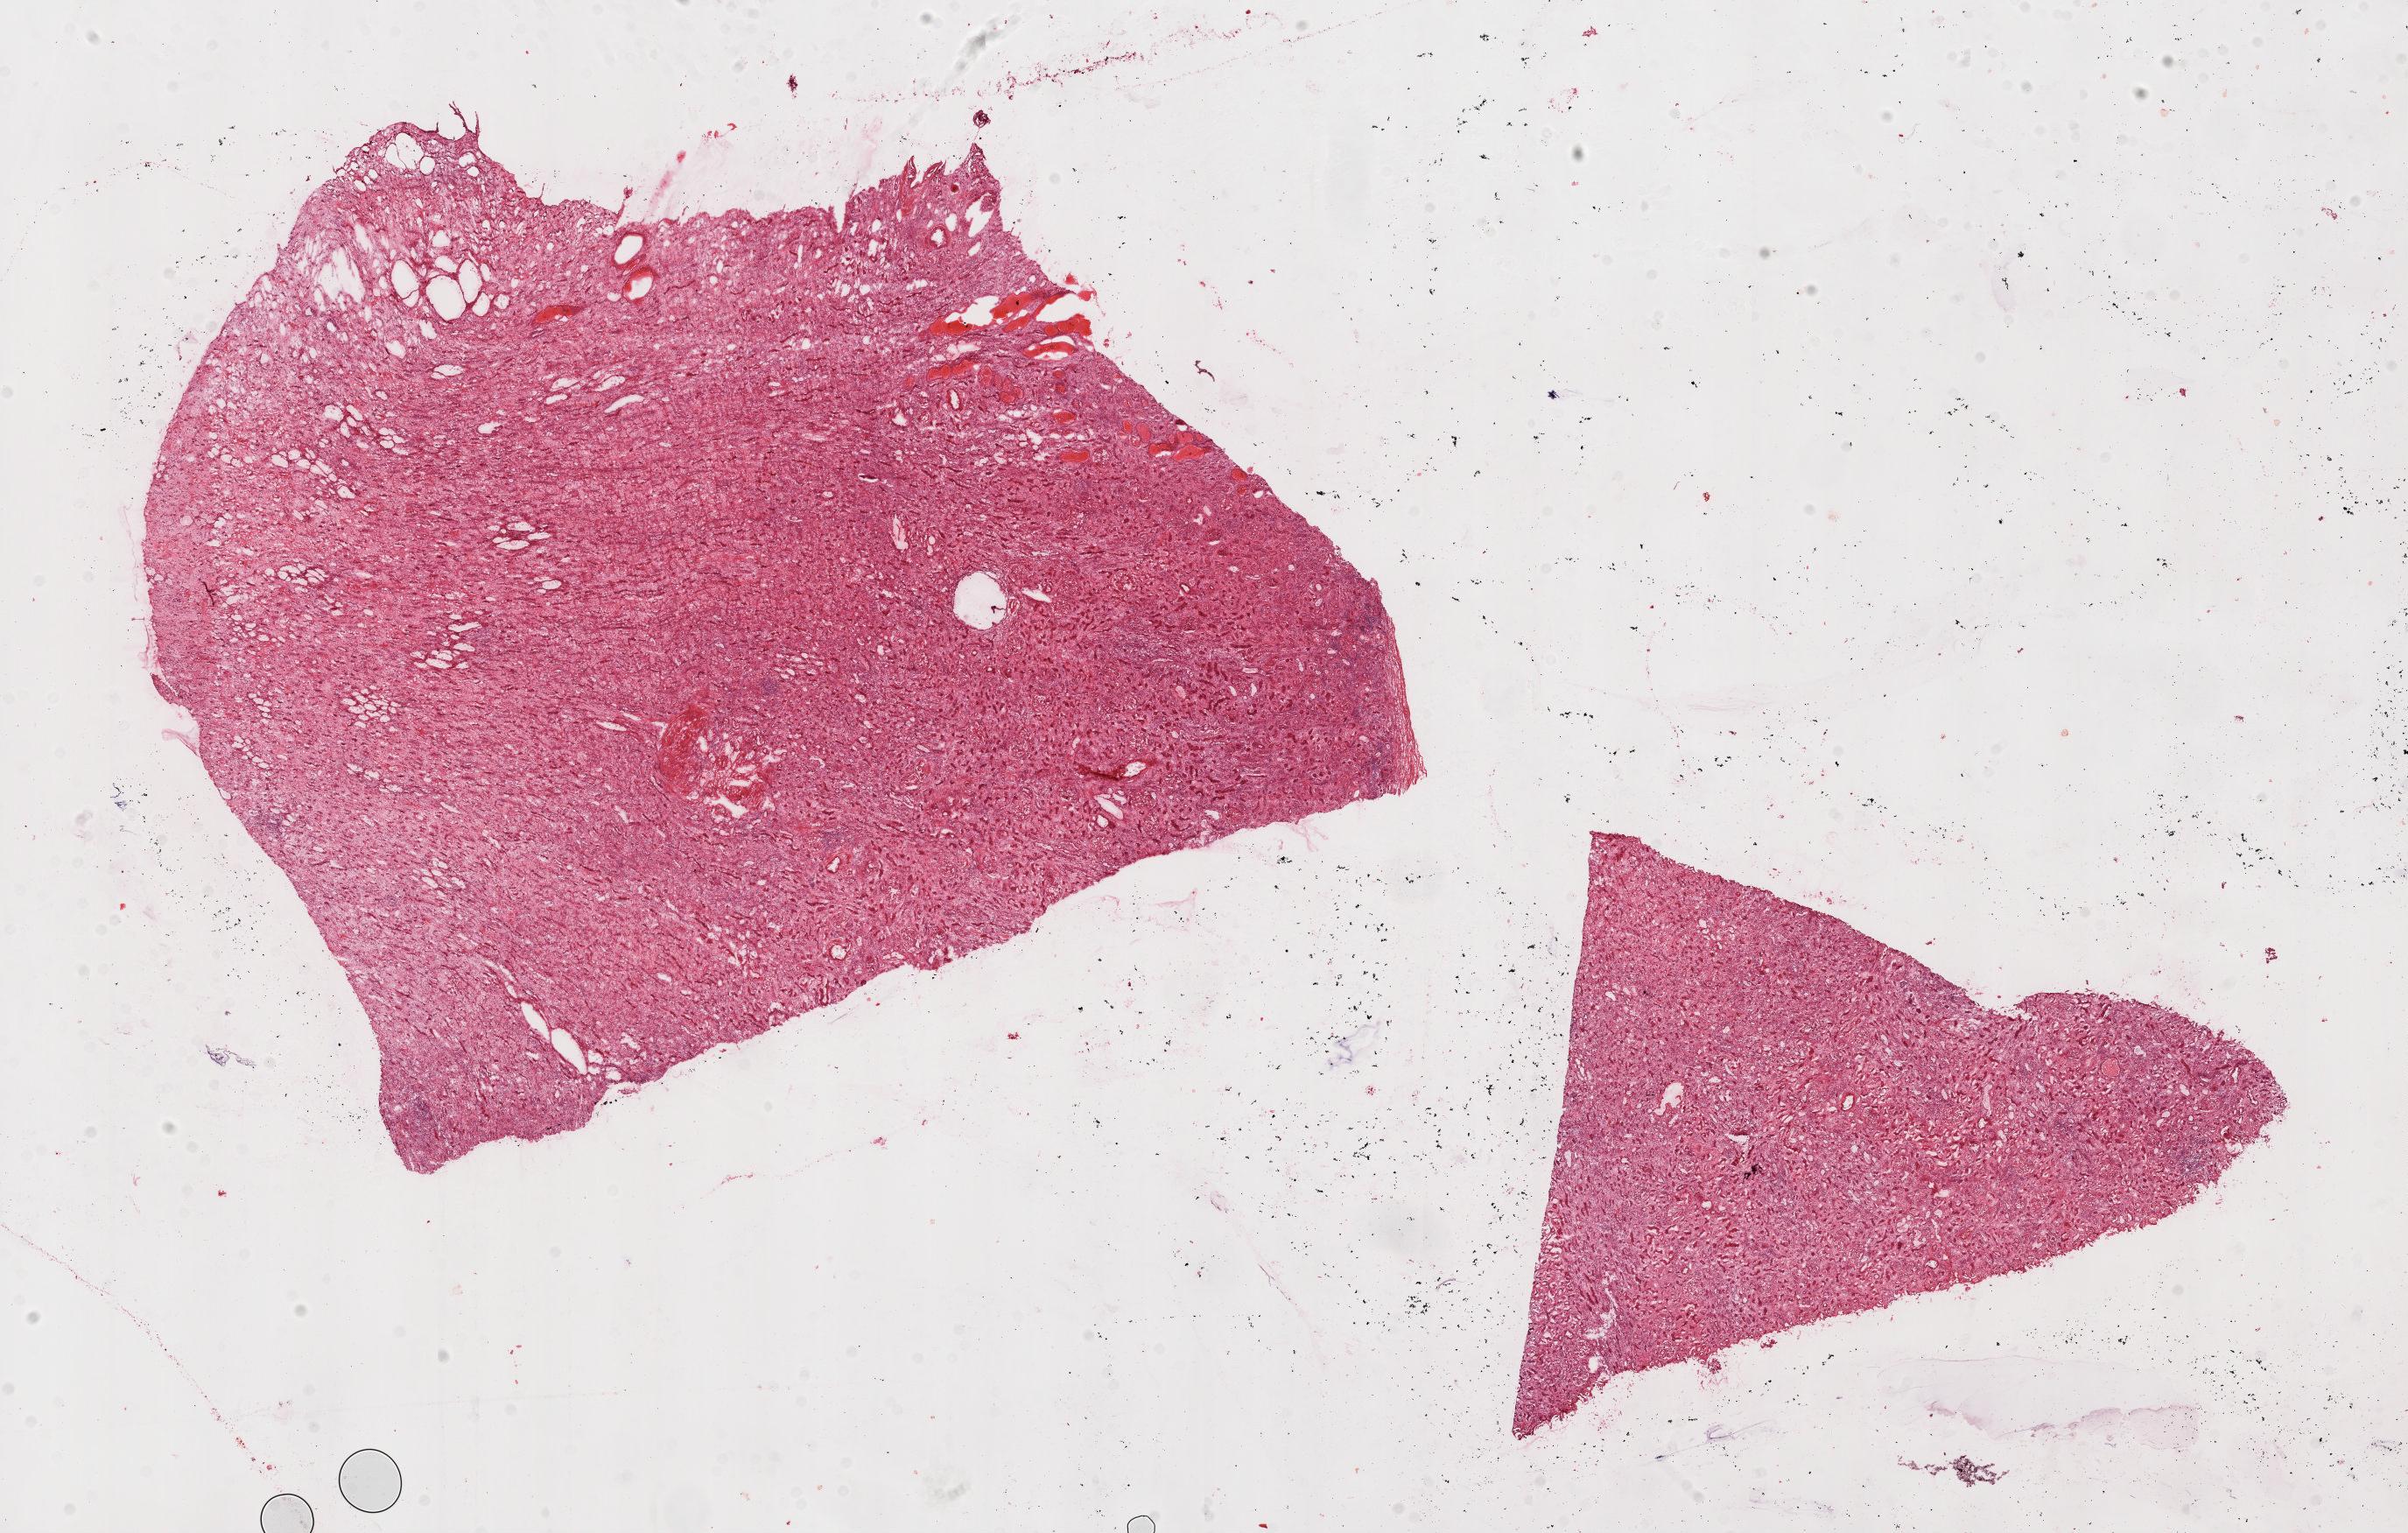
Whole-slide histology image, H&E, shown as a low-resolution overview of the whole scanned area (about 21.8 x 13.9 mm, slide scanned at 20x), frozen section from the top of the tissue portion, kidney, solid tissue normal (non-tumour tissue) sample. Male patient; age at initial diagnosis 65 years.
- this section: solid tissue normal sample (biorepository sample class)
- patient diagnosis: Clear cell adenocarcinoma, NOS